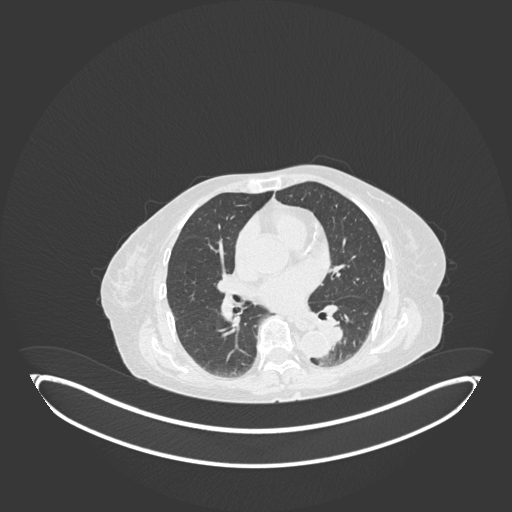
Chest CT, one axial slice. Position 59 of 189 along the scan axis. Reconstruction kernel B30f. 120 kVp. Lung window (W 1500 / L -600 HU). 512 × 512 image matrix, field of view 500 × 500 mm. Female patient, age 82 years. Case-level facts recorded for this patient, not image findings: clinical TNM (as recorded): T1b N0 M1.
Outlined on this slice (bounding box drawn by a radiologist):
- lung tumour (recorded histology: adenocarcinoma): bounding box <314,315,345,346> (left, top, right, bottom; pixels)